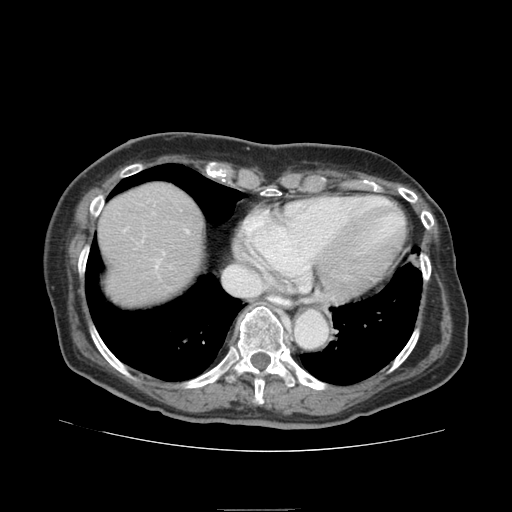
Contrast-enhanced abdominal CT (liver protocol), one axial slice. Position 74 of 95 along the scan axis. Reconstruction kernel STANDARD. 140 kVp. Soft-tissue window (W 400 / L 40 HU). 2.5 mm slice thickness. 512 × 512 image matrix, field of view 360 × 360 mm. Case-level facts recorded for this patient, not image findings: diagnosis: hepatocellular carcinoma (patient treated with transarterial chemoembolisation; whether this scan precedes or follows treatment is not stated here); TNM stage (as recorded): Stage-IVA; Child-Pugh class: B; tumour nodularity: uninodular.
Outlined on this slice (semi-automatically segmented with operator editing):
- abdominal aorta: bounding box (x1, y1, x2, y2) in pixels: (296, 309, 327, 348)
- liver parenchyma outside the tumour (the mass and vessels are separate outlines, so this box may not span the whole liver): (98, 182, 204, 304)
- liver vessels: (156, 230, 189, 268)